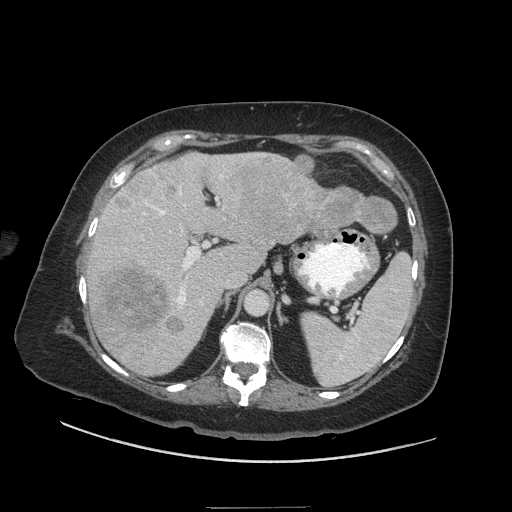
Contrast-enhanced abdominal CT (liver protocol), one axial slice. Position 31 of 81 along the scan axis. 140 kVp. Soft-tissue window (W 400 / L 40 HU). 2.5 mm slice thickness. 512 × 512 image matrix, field of view 440 × 440 mm. Case-level facts recorded for this patient, not image findings: diagnosis: hepatocellular carcinoma (patient treated with transarterial chemoembolisation; whether this scan precedes or follows treatment is not stated here); TNM stage (as recorded): Stage-II; Child-Pugh class: A; tumour differentiation: moderately differentiated; tumour nodularity: multinodular.
Annotated regions visible in this slice (semi-automatic segmentation, software-assisted and operator-edited):
- liver parenchyma outside the tumour (the mass and vessels are separate outlines, so this box may not span the whole liver): bounding box [x1, y1, x2, y2] px = [88, 152, 345, 374]
- mass: [92, 154, 398, 340]
- liver vessels: [103, 157, 230, 310]